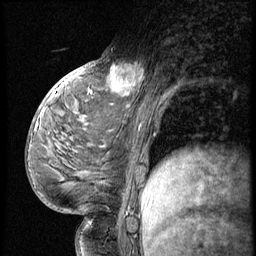
Breast MRI (dynamic contrast-enhanced), one sagittal slice; position 30 of 56 along the scan axis; 3 images stored at this slice position (order not interpretable as contrast timing); 1.5 T; TE 4.2 ms, TR 9 ms; 256 × 256 image matrix. Patient: female, 54 years. From the clinical record (not read from this slice): setting: breast cancer imaged before/during neoadjuvant chemotherapy; receptor status: triple-negative.
Structures marked on this image (semi-automatically segmented with operator editing):
- analysis volume of interest (the breast-tissue region the enhancement analysis was run in; not a lesion): bounding box (x1, y1, x2, y2) in pixels: (99, 53, 149, 102)
- tumour enhancement mask (voxels above the 140 % enhancement threshold inside the analysis volume of interest): (110, 63, 144, 95)